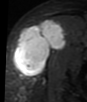
MRI of an extremity soft-tissue mass, one axial slice. Slice 27 of 48 in the series (ordered by position). STIR. MR volume resampled by the dataset authors to the PET/CT grid (not the native acquisition matrix). 3.27 mm slice thickness. 87 × 102 image matrix. Female patient. Case-level facts recorded for this patient, not image findings: histological type: synovial sarcoma; grade: intermediate; site of the primary tumour: right thigh.
Outlined on this slice (expert contour drawn on MRI and transferred to this co-registered scan by the dataset authors):
- gross tumour volume including surrounding oedema: box from (x=13, y=20) to (x=66, y=78) px
- gross tumour volume (mass): (x=13, y=20)–(x=66, y=76)